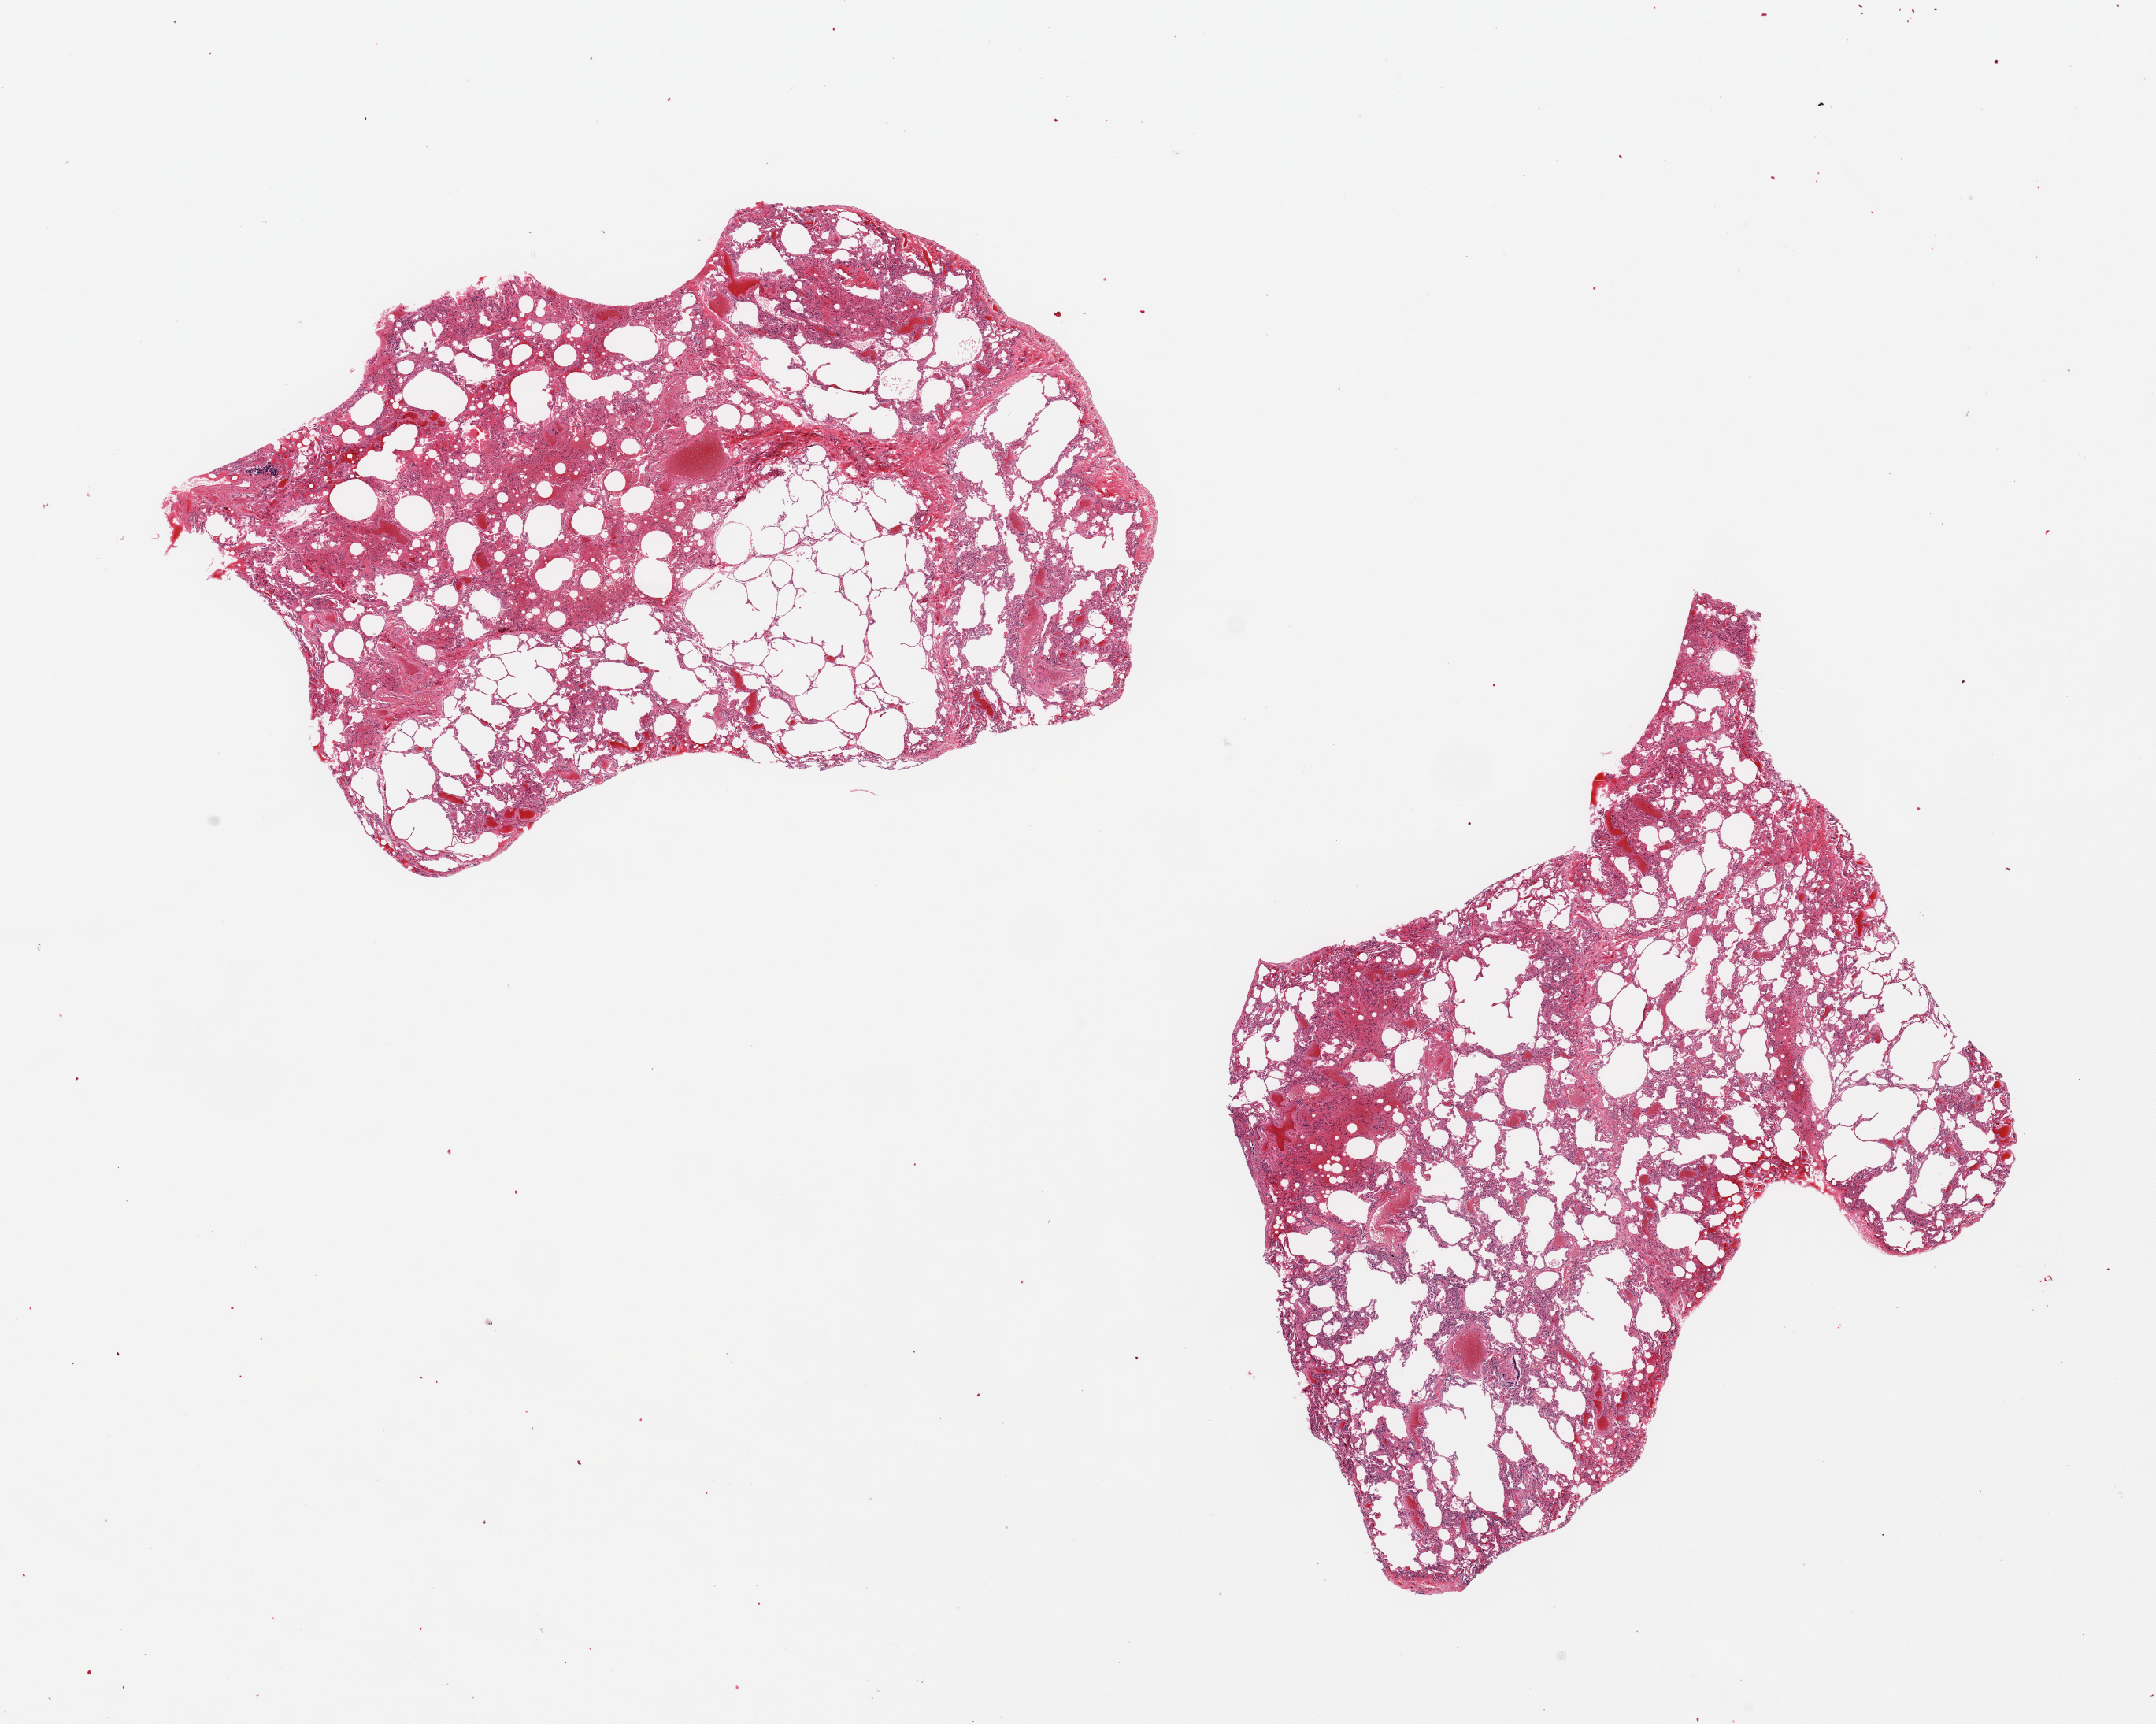
Haematoxylin and eosin whole-slide image, brightfield, shown as a low-resolution overview of the whole scanned area (about 21.7 x 17.3 mm, slide scanned at 20x), PAXgene-fixed paraffin-embedded (PFPE) section, target tissue: lung, donor tissue sample. Donor sex: male.
Review note (as recorded): 2 pieces ~7x7mm. Poorly preserved, moderate congestion, areas of emphysematous change noted.